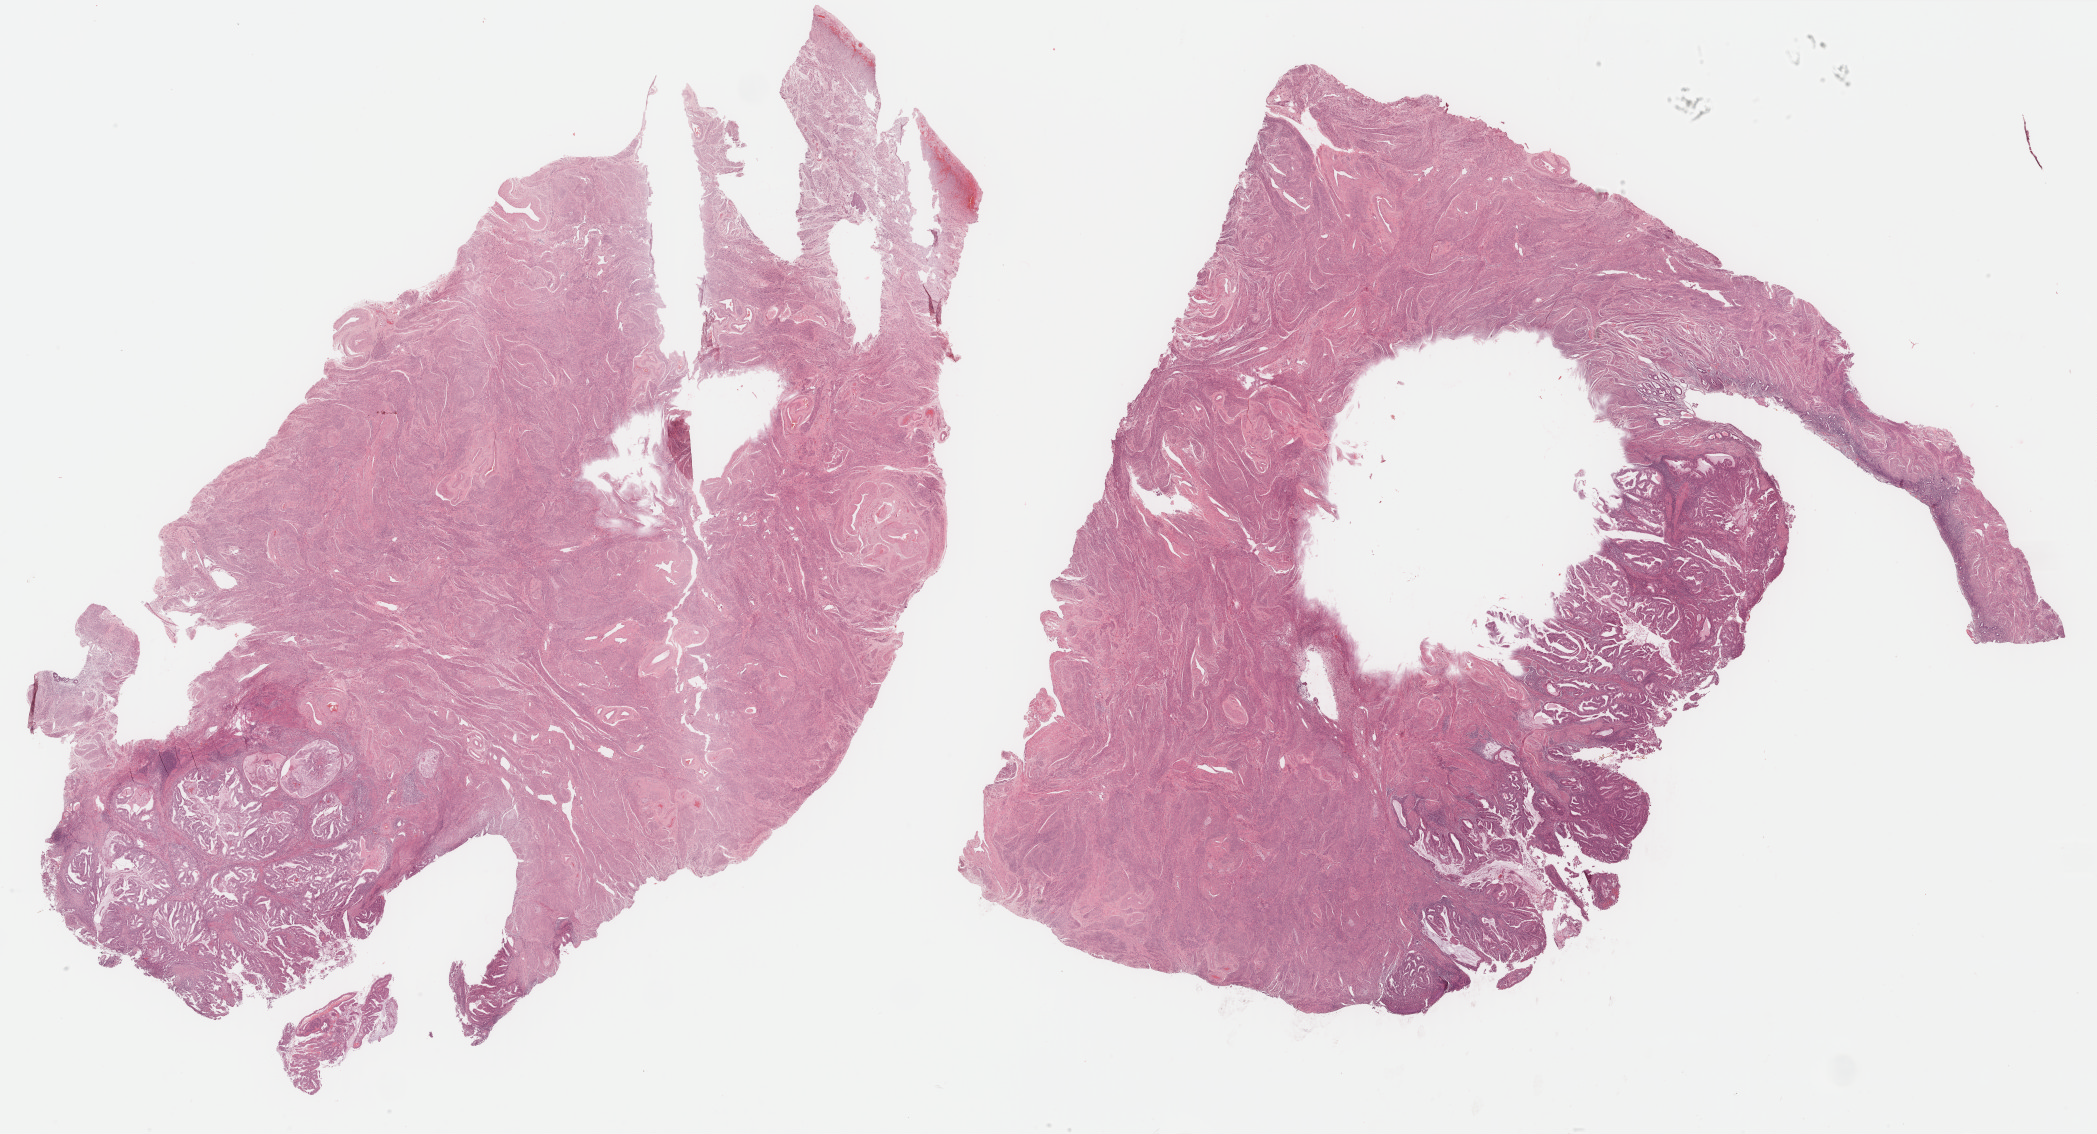
H&E-stained whole-slide image, low-resolution overview of the scanned area, about 33.3 x 18.0 mm (slide scanned at 40x); FFPE section; primary tumour sample from the uterus. Female patient; age at initial diagnosis 54 years. Histologic grade: G1 (well differentiated).
• histologic diagnosis: Endometrioid adenocarcinoma, NOS (endometrium)
• FIGO stage: IA